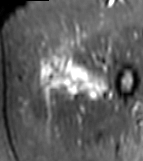
MRI of an extremity soft-tissue mass, one axial slice; position 16 of 81 along the scan axis; STIR; MR volume resampled by the dataset authors to the PET/CT grid (not the native acquisition matrix); 3.27 mm slice thickness; 143 × 161 image matrix, field of view 140 × 157 mm. Female patient. From the clinical record (not read from this slice): histological type: myxofibrosarcoma; grade: intermediate; site of the primary tumour: left thigh.
Annotated regions visible in this slice (expert contour drawn on MRI and transferred to this co-registered scan by the dataset authors):
- gross tumour volume including surrounding oedema: box from (x=35, y=55) to (x=111, y=104) px
- gross tumour volume (mass): (x=45, y=55)–(x=100, y=89)